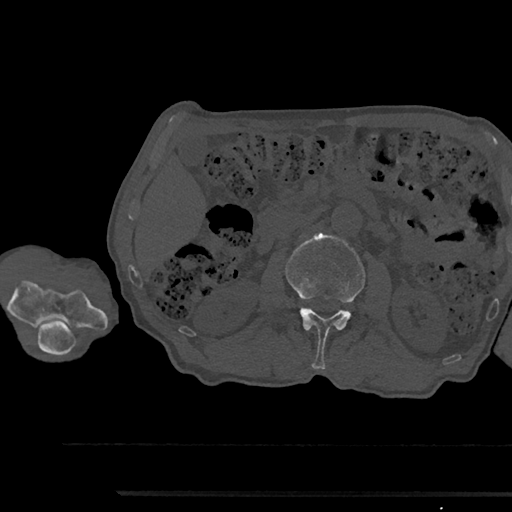
CT including the spine, one axial slice. Slice 558 of 797 in the series (ordered by position). Bone window (W 1800 / L 400 HU). 512 × 512 image matrix, field of view 367 × 367 mm. Patient: male, 79 years. From the clinical record (not read from this slice): primary cancer: prostate.
Annotated regions visible in this slice (semi-automatic segmentation, software-assisted and operator-edited):
- L2 vertebra: bounding box (x1, y1, x2, y2) in pixels: (285, 233, 366, 369)